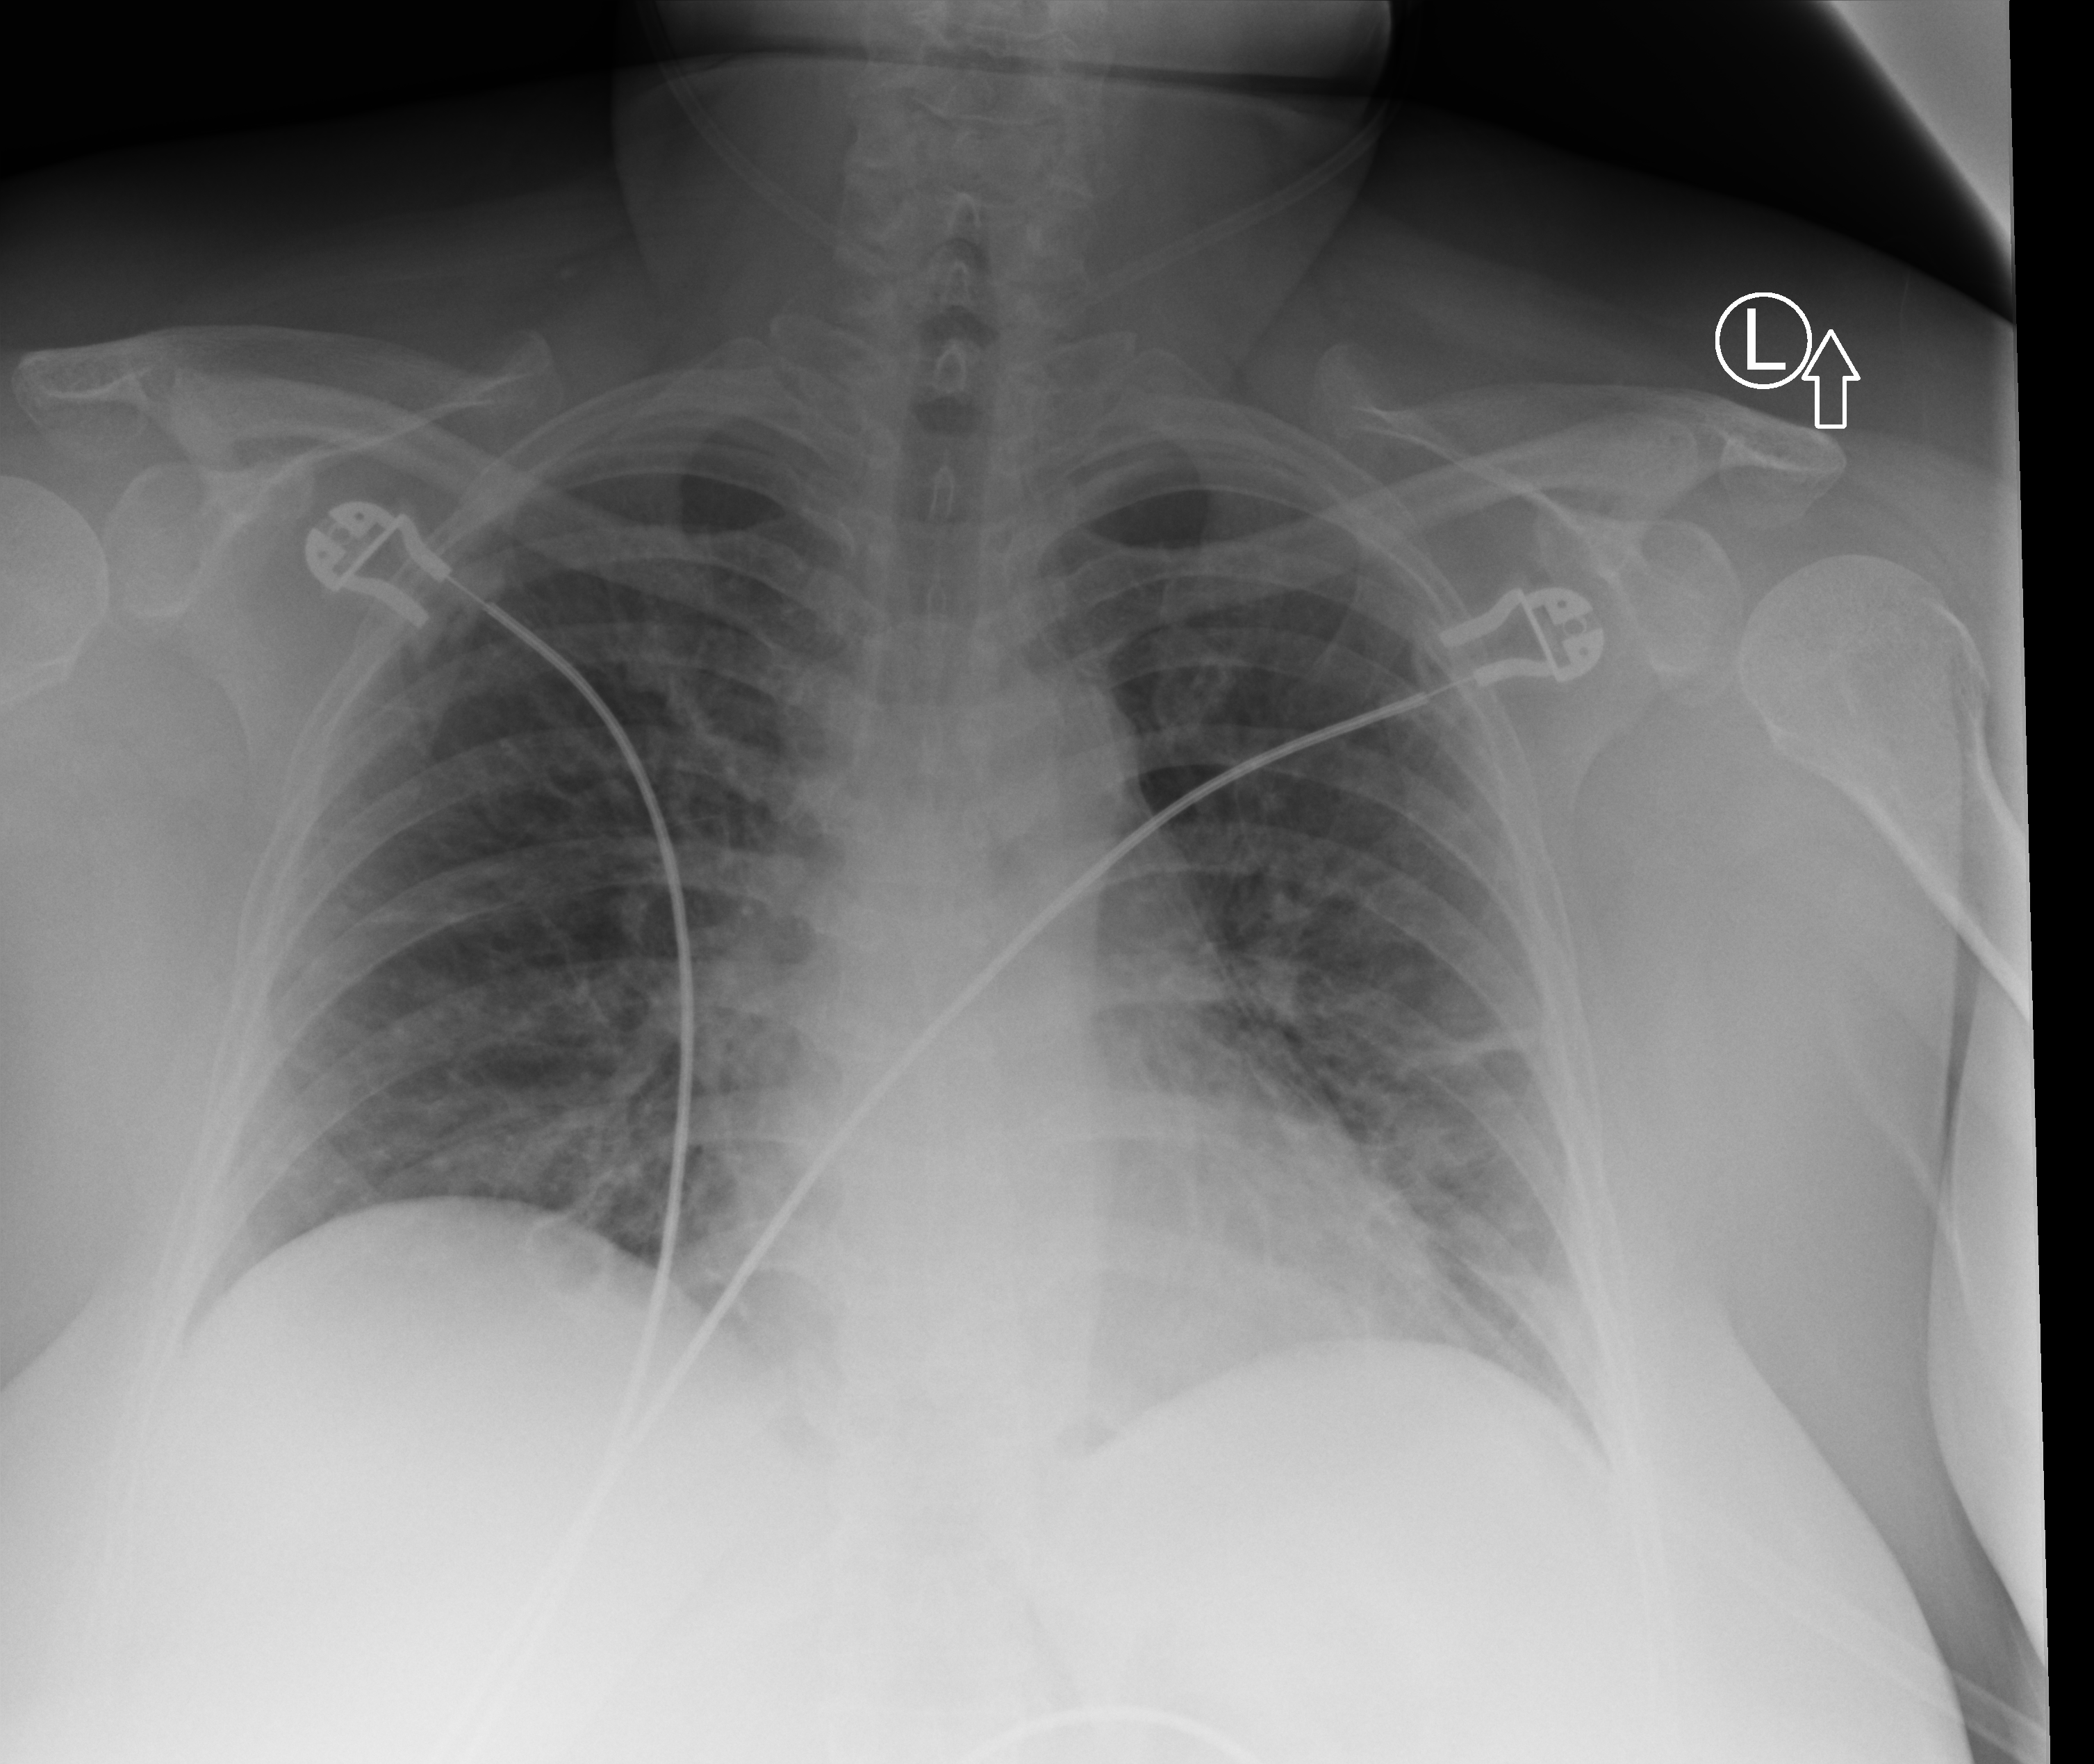
Chest X-ray (portable). Female patient hospitalised with COVID-19, age 18–59 years.
From the hospital-stay record, not from the radiograph (when in the stay this image was taken is not recorded): mechanically ventilated during this hospital stay: no.